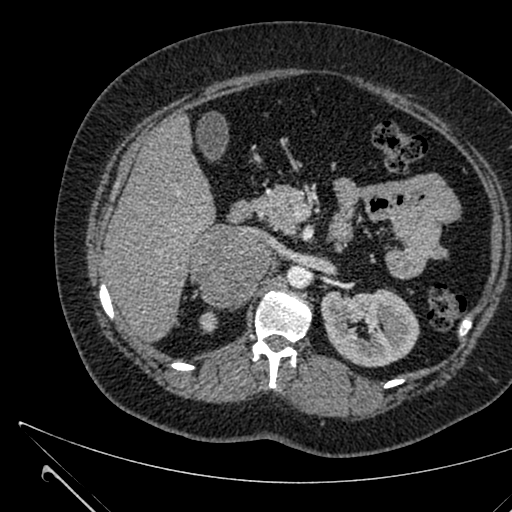
Contrast-enhanced abdominal CT, one axial slice; slice 392 of 731 in the series (ordered by position); 120 kVp; intravenous contrast given; soft-tissue window (W 400 / L 40 HU); 512 × 512 image matrix, field of view 376 × 376 mm. Female patient, age 36 years. From the clinical record (not read from this slice): diagnosis: adrenocortical carcinoma; tumour side: right adrenal; tumour size at pathology: 10 cm; Ki-67 index: 20 %; stage (as recorded): 4.
Outlined on this slice (semi-automatically segmented with operator editing):
- mass: bounding box [x1, y1, x2, y2] px = [191, 225, 266, 306]